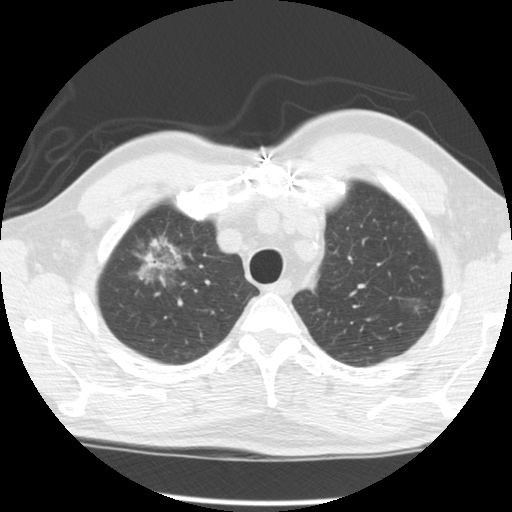
Chest CT (low-dose screening protocol), one axial image; second screening round (one year after baseline); lung window (W 1500 / L -600 HU); 2.5 mm slice thickness; 120 kVp. Male, age 64 years at enrolment. Former smoker at enrolment.
• Lesion marked by an expert reader, bounding box [x1, y1, x2, y2] px = [121, 226, 199, 299].
• The screening reader recorded 2 non-calcified nodules or masses ≥4 mm on this exam; which of them this box marks is not recorded.
• Official screen result: positive, other.
• Participant outcome: lung cancer diagnosed 429 days after this screen (after the third annual screen) — adenocarcinoma, NOS, right upper lobe, well differentiated (G1), stage IB (AJCC 6th edition), 45 mm at pathology.